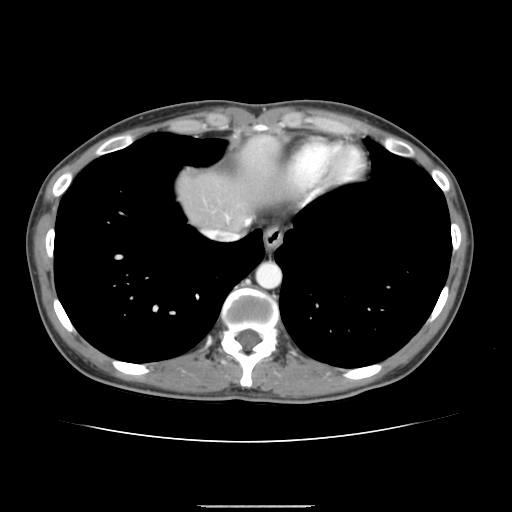
Contrast-enhanced abdominal CT, one axial slice. Position 134 of 150 along the scan axis. 120 kVp. Intravenous contrast given. Soft-tissue window (W 400 / L 40 HU). 2.5 mm slice thickness. 512 × 512 image matrix, field of view 324 × 324 mm. Female patient, age 32 years. Case-level facts recorded for this patient, not image findings: diagnosis: colorectal cancer liver metastases, imaged before liver resection; multiple liver metastases: yes; largest metastasis: 0.7 cm; chemotherapy before resection: yes.
Annotated regions visible in this slice (outlined manually by an expert reader):
- hepatic veins: bounding box <204,220,249,240> (left, top, right, bottom; pixels)
- liver: <178,175,268,229>
- planned liver remnant (the part of the liver to remain after resection): <178,174,264,230>